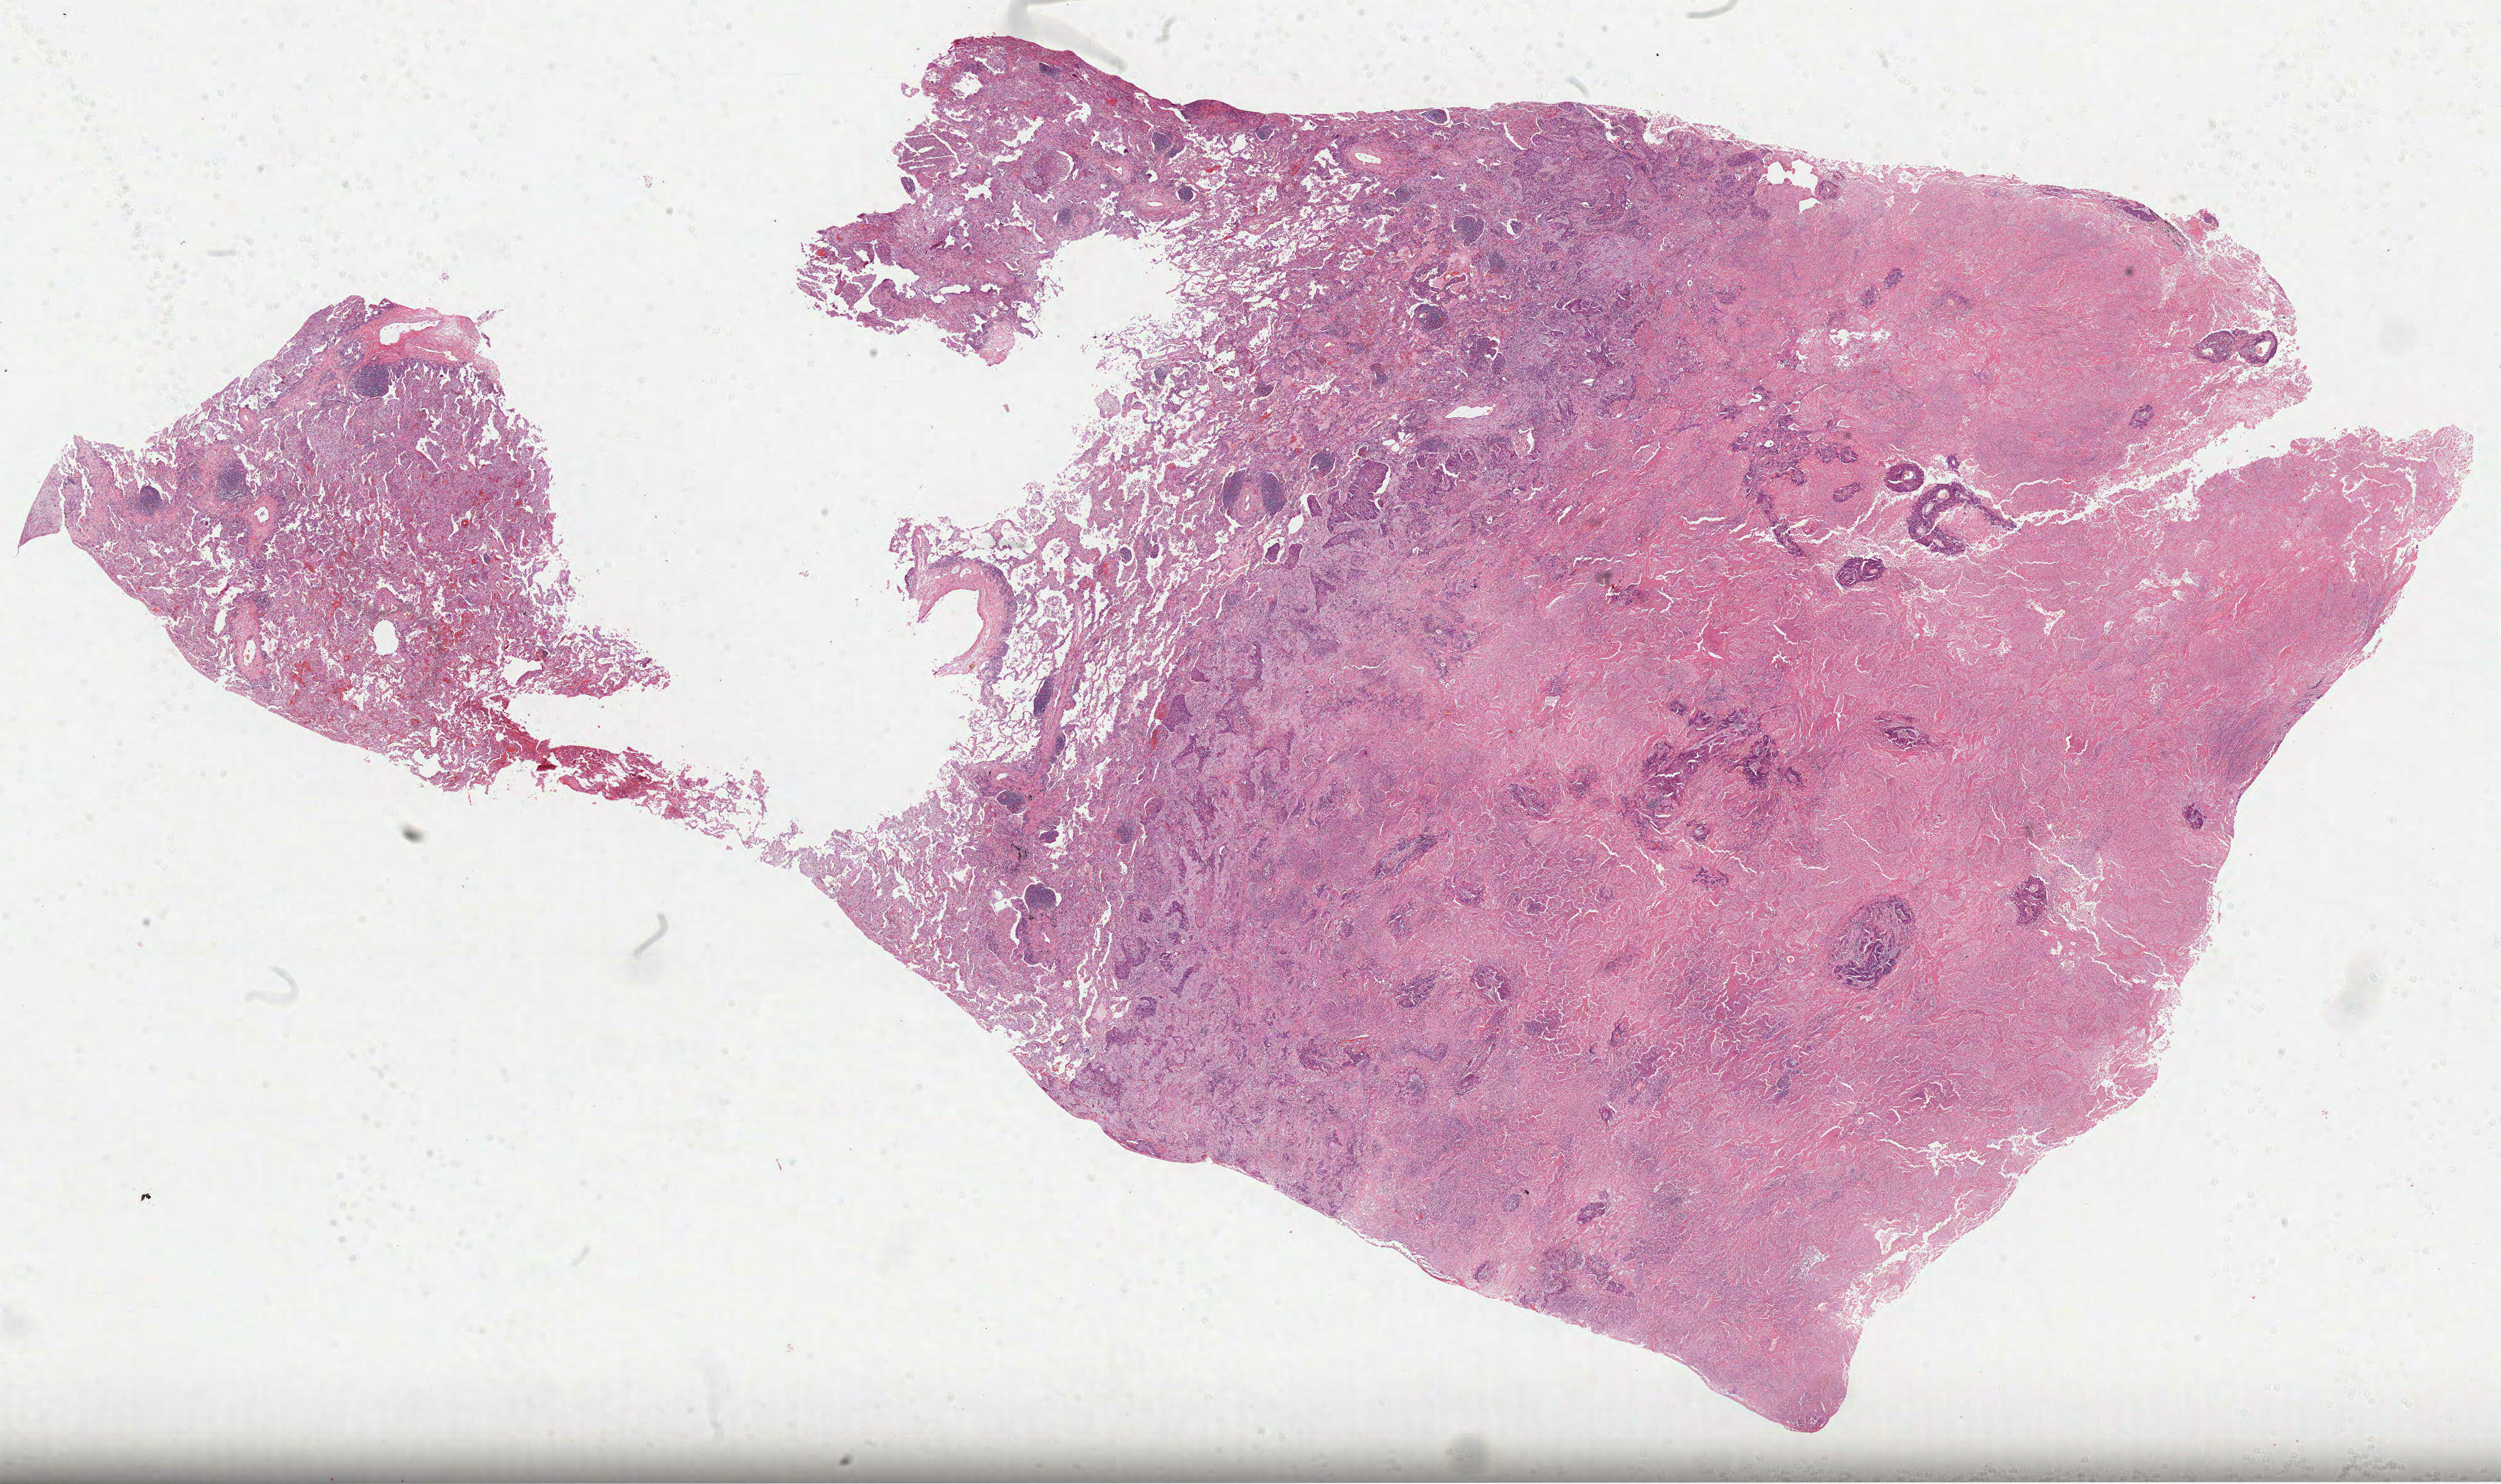
Digitized H&E-stained tissue section (whole slide), a low-resolution overview of the entire scanned area, about 32.4 x 19.2 mm (slide scanned at 40x), FFPE section, primary tumour sample from the lung. Male patient; age at initial diagnosis 73 years.
- laterality: right
- pathologic diagnosis: Squamous cell carcinoma, NOS
- AJCC pathologic stage: IIB